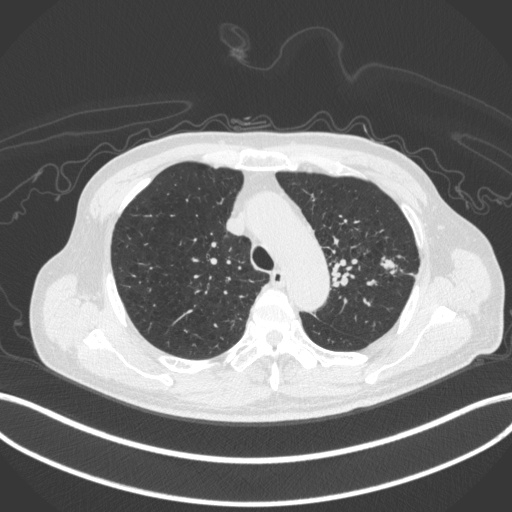
Chest CT, one axial slice. Slice 330 of 420 in the series (ordered by position). Reconstruction kernel B31f. Lung window (W 1500 / L -600 HU). 512 × 512 image matrix. Male patient, age 77 years. Case-level facts recorded for this patient, not image findings: clinical TNM (as recorded): T3 N1 M0.
Outlined on this slice (rectangle marked by the reading radiologist):
- lung tumour (recorded histology: adenocarcinoma): bounding box (x1, y1, x2, y2) in pixels: (382, 251, 398, 274)